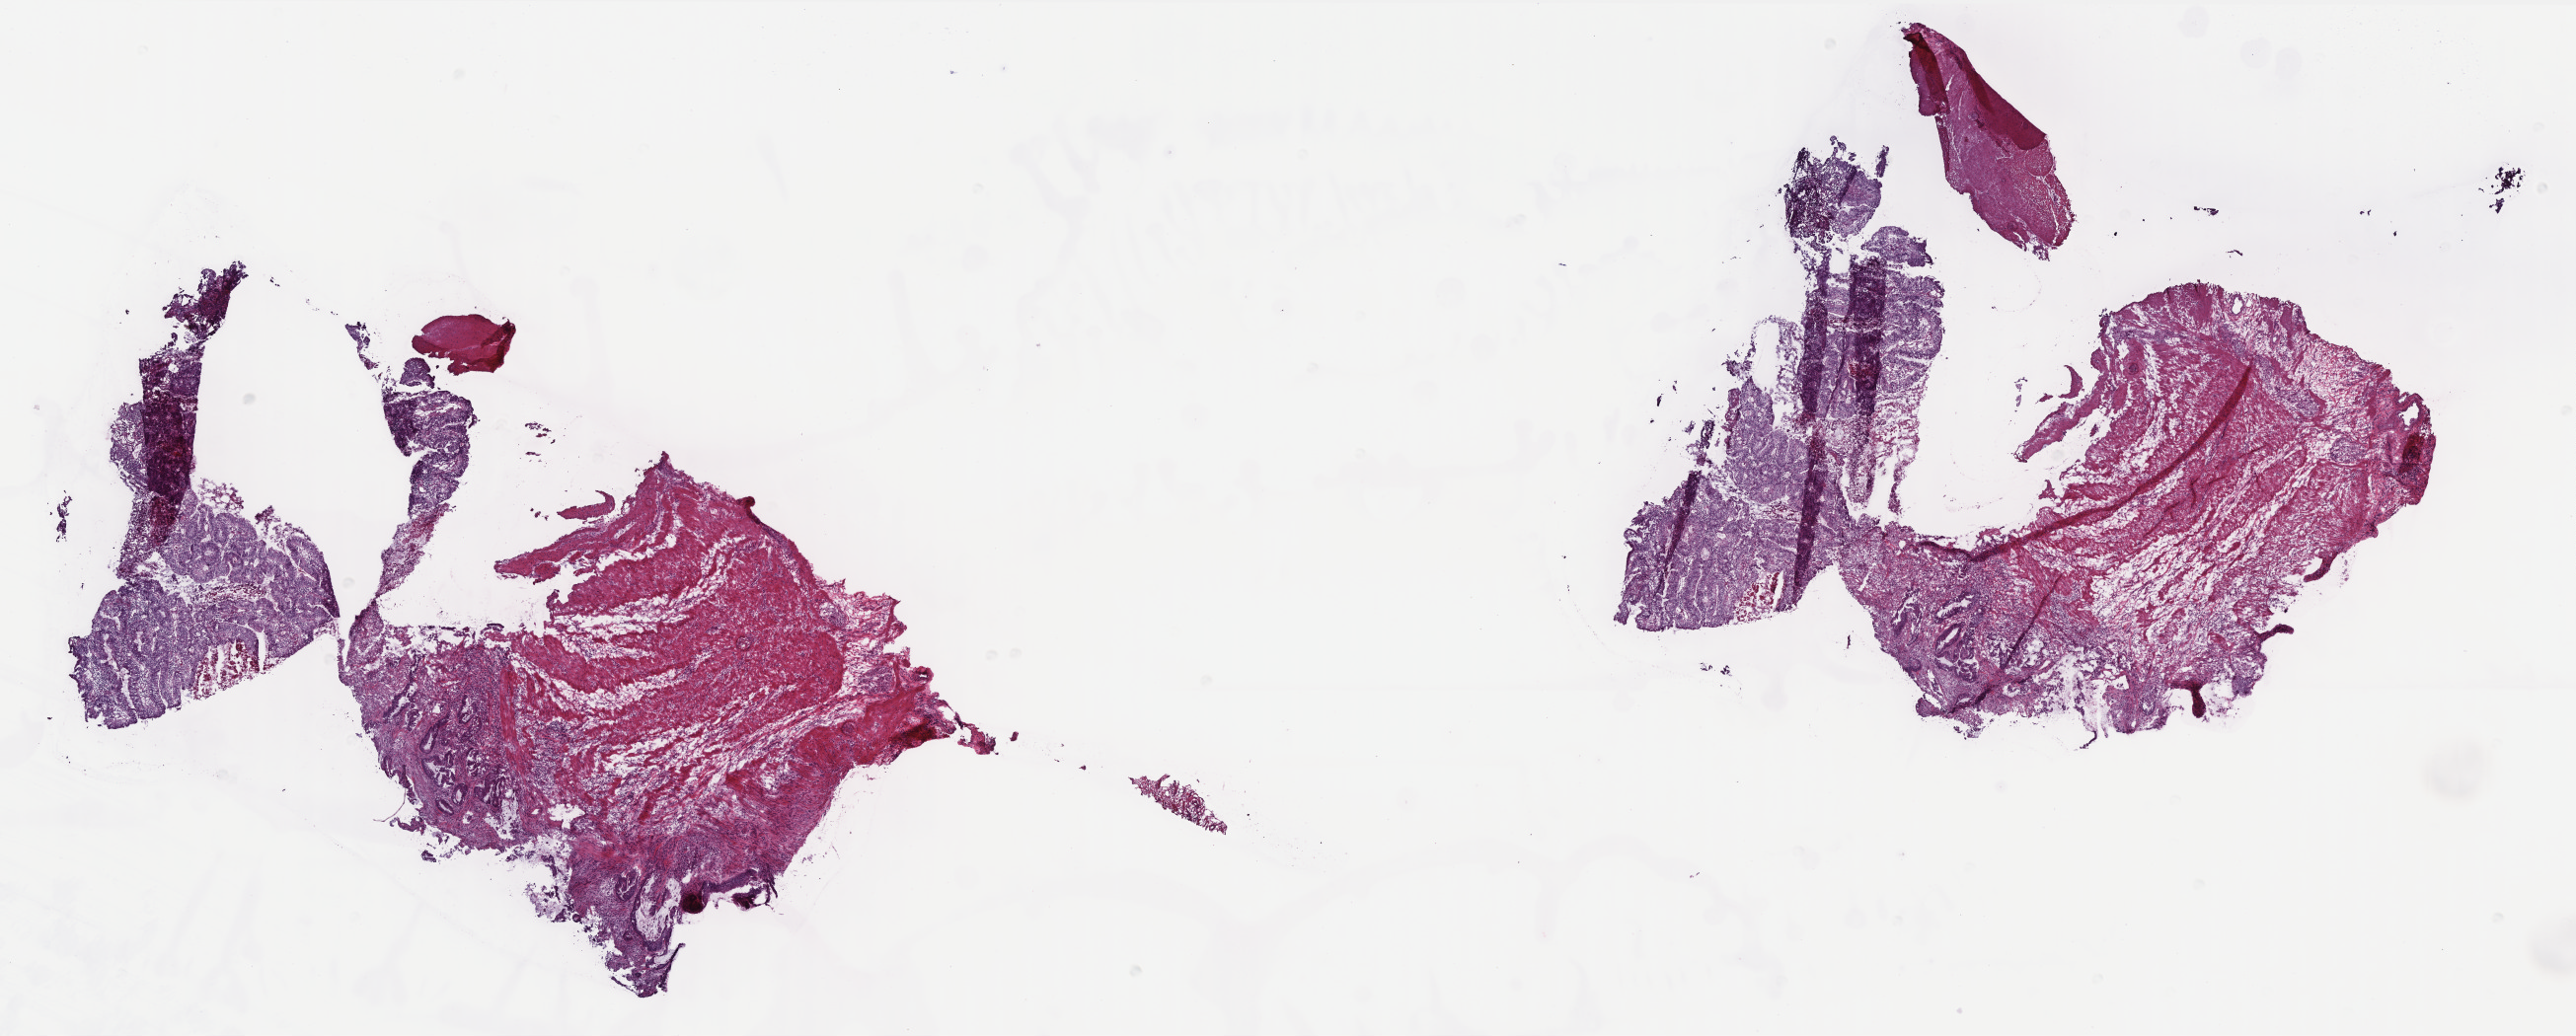
Digitized Hematoxylin and eosin (H&E) stained tissue section (whole slide) — a low-resolution overview of the entire scanned area, about 20.9 x 8.4 mm, frozen section from the bottom of the tissue portion, sample: primary tumour, colon. Patient: male, age at initial diagnosis 79 years. Pathologist review of this section (percent, as recorded): tumour cells 40%, tumour nuclei 70%, normal cells 50%, stromal cells 9%, necrosis 1%. Infiltration values recorded for this section: lymphocyte infiltration 6%, monocyte infiltration 3%, neutrophil infiltration 12%.
Lymph nodes positive (case pathology): 0 of 55 examined. Pathologic diagnosis: Adenocarcinoma, NOS (sigmoid colon). AJCC pathologic stage: IIA (6th edition).